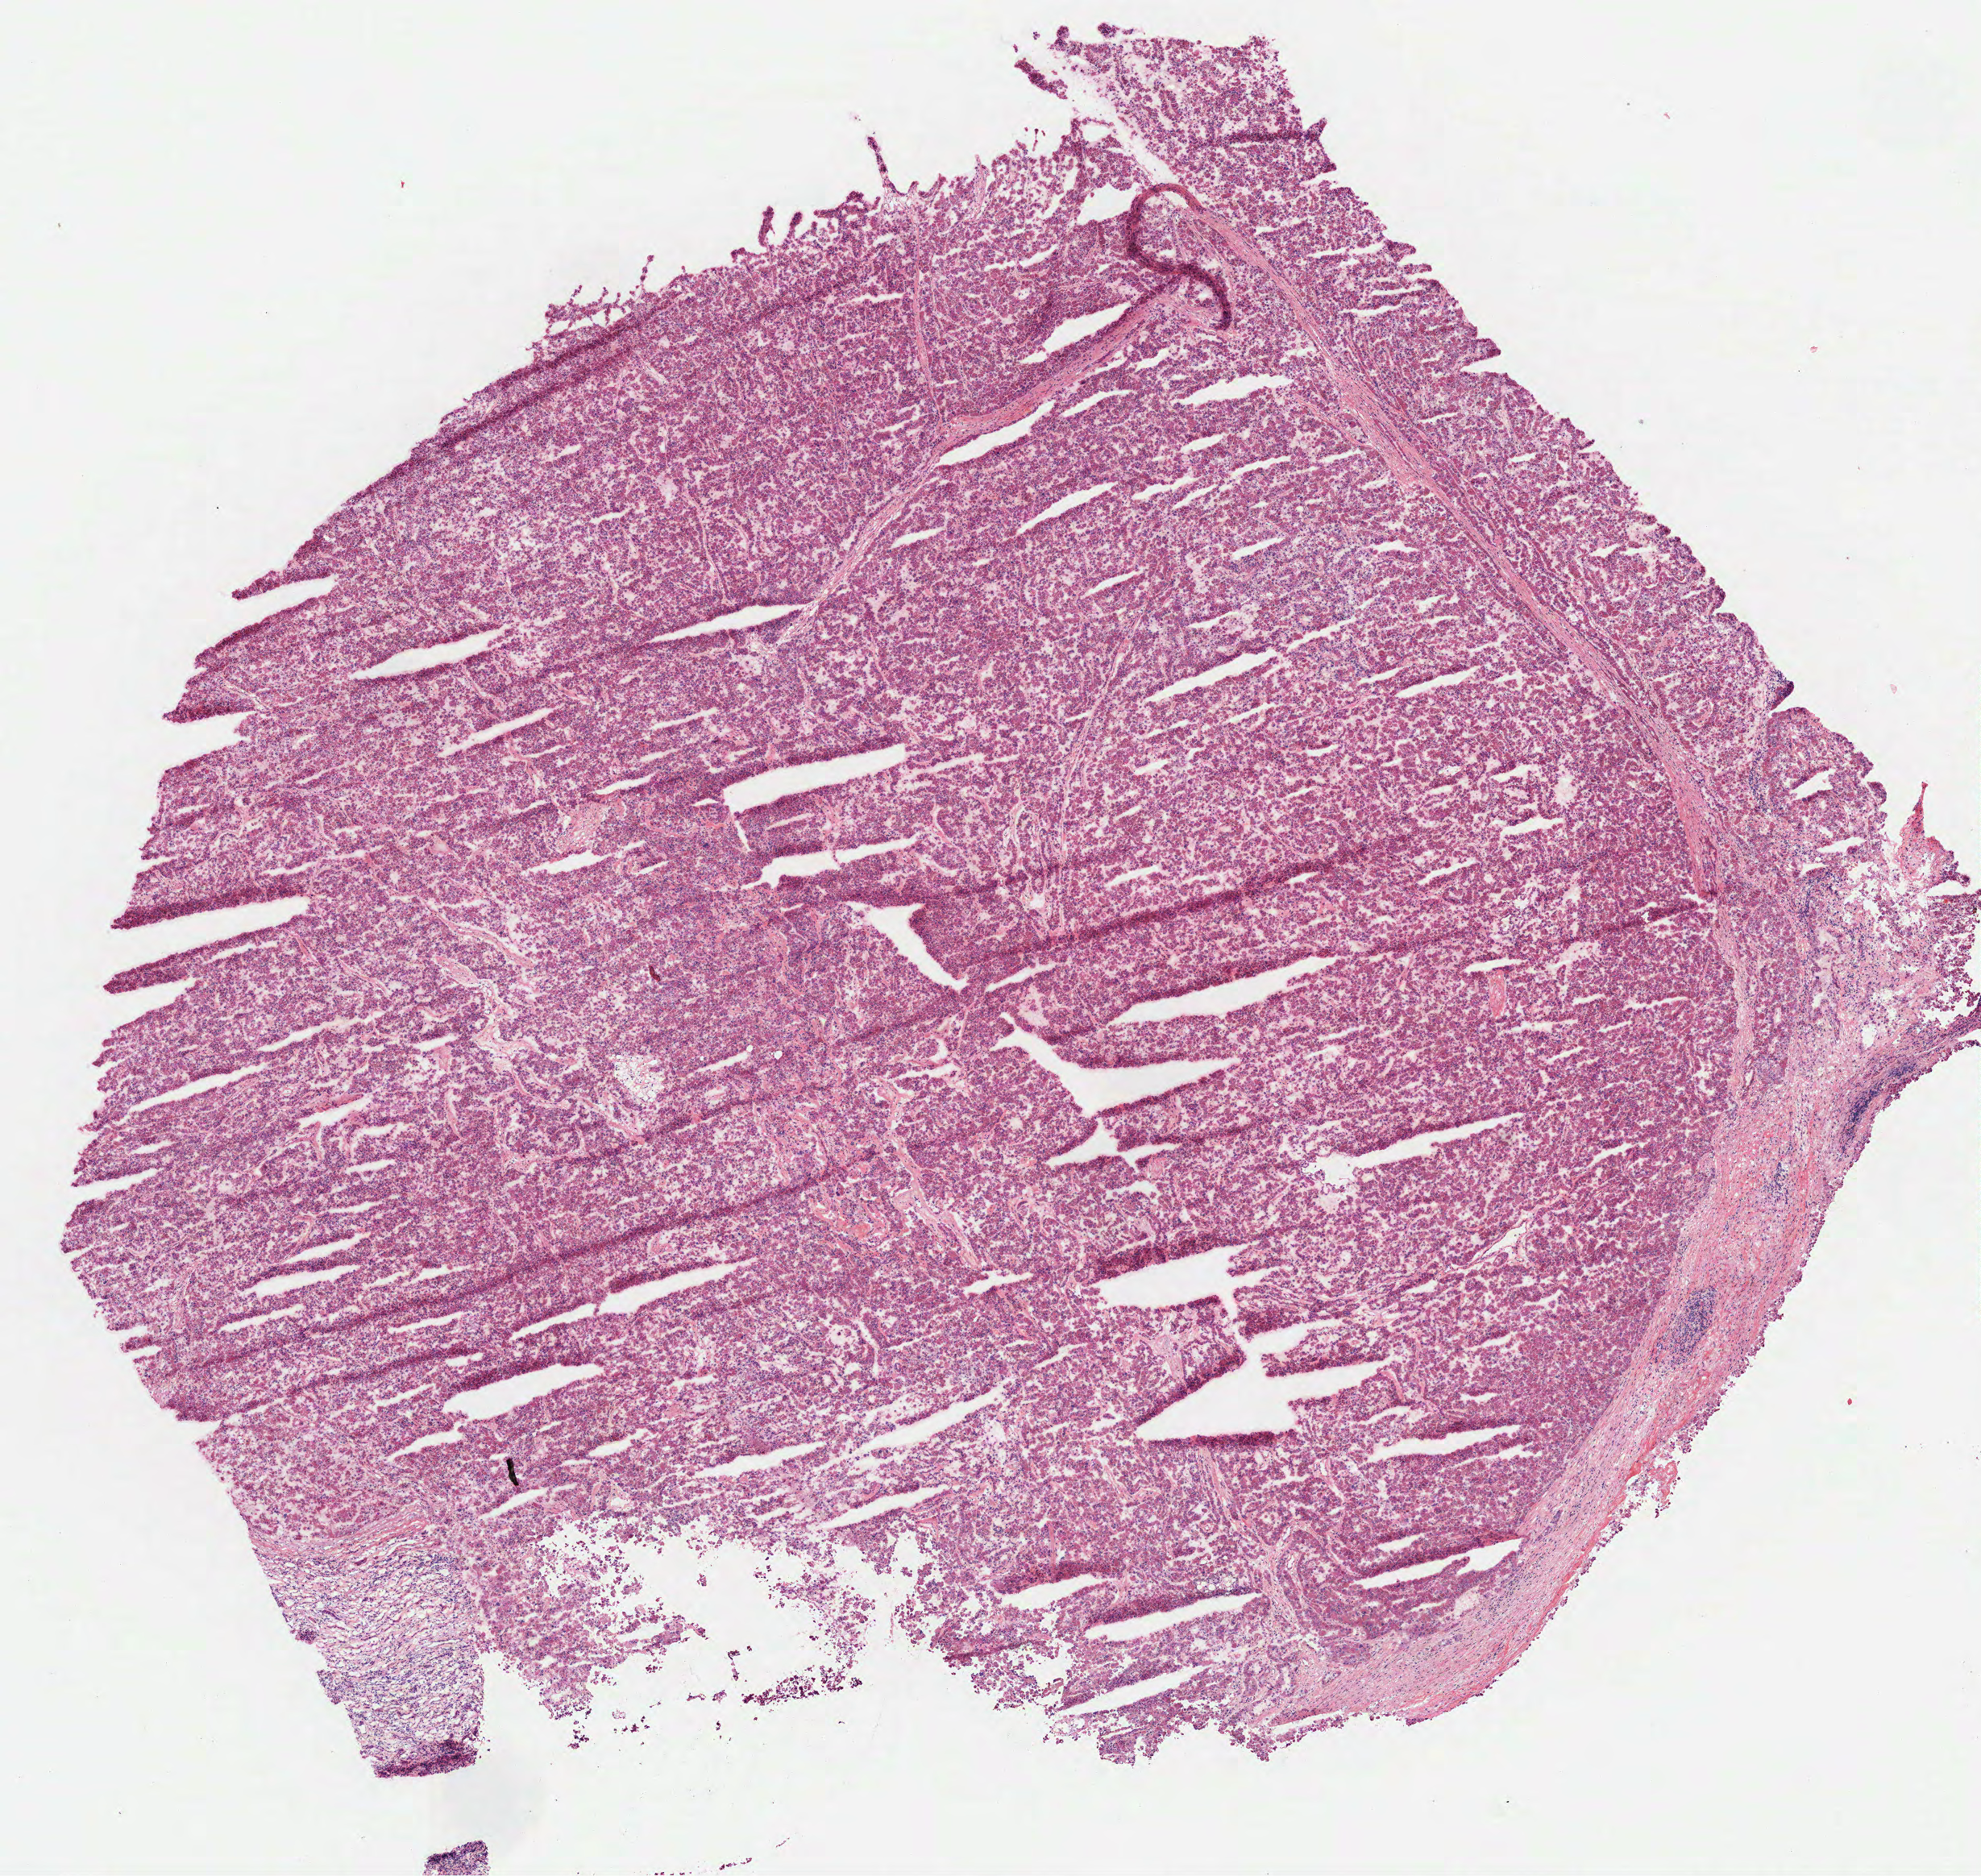
H&E whole-slide image — a low-resolution overview of the entire scanned area, about 9.9 x 9.4 mm (from a 40x scan), frozen section from the top of the tissue portion, primary tumour sample from the kidney. Male, age 81 years at initial diagnosis. Pathologist review of this section (percent, as recorded): tumour cells 100%, tumour nuclei 90%, normal cells 0%, stromal cells 0%, necrosis 0%. Inflammatory infiltration, as recorded: lymphocyte infiltration 2%, monocyte infiltration 0%, neutrophil infiltration 0%.
- diagnosis: Papillary adenocarcinoma, NOS
- lymph nodes positive (case pathology): 3 of 8 examined
- AJCC pathologic stage: III (7th edition)